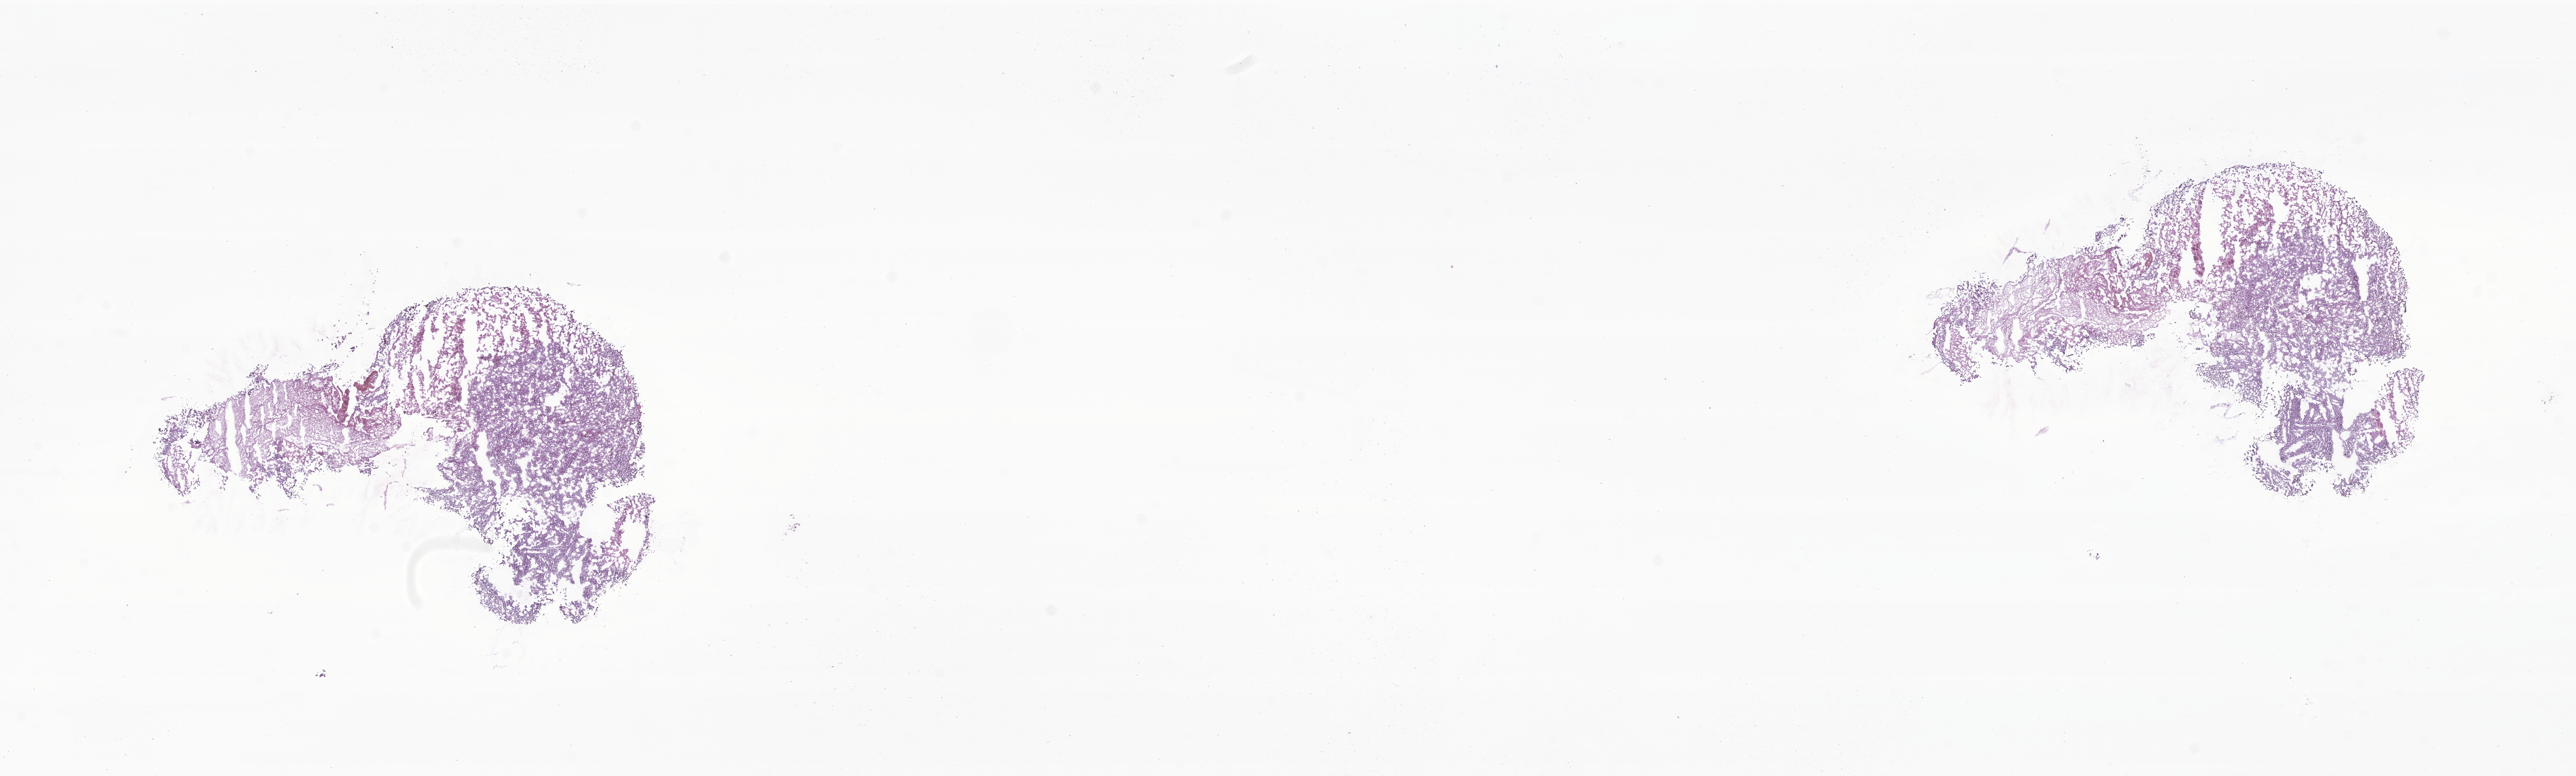
Whole-slide image, hematoxylin and eosin (H&E) stain of tumor tissue from the brain, low-resolution overview of the scanned area, about 31.0 x 9.3 mm. Frozen section (OCT-embedded). Patient male; age 168 days.
Diagnosis: Atypical teratoid/rhabdoid tumor.